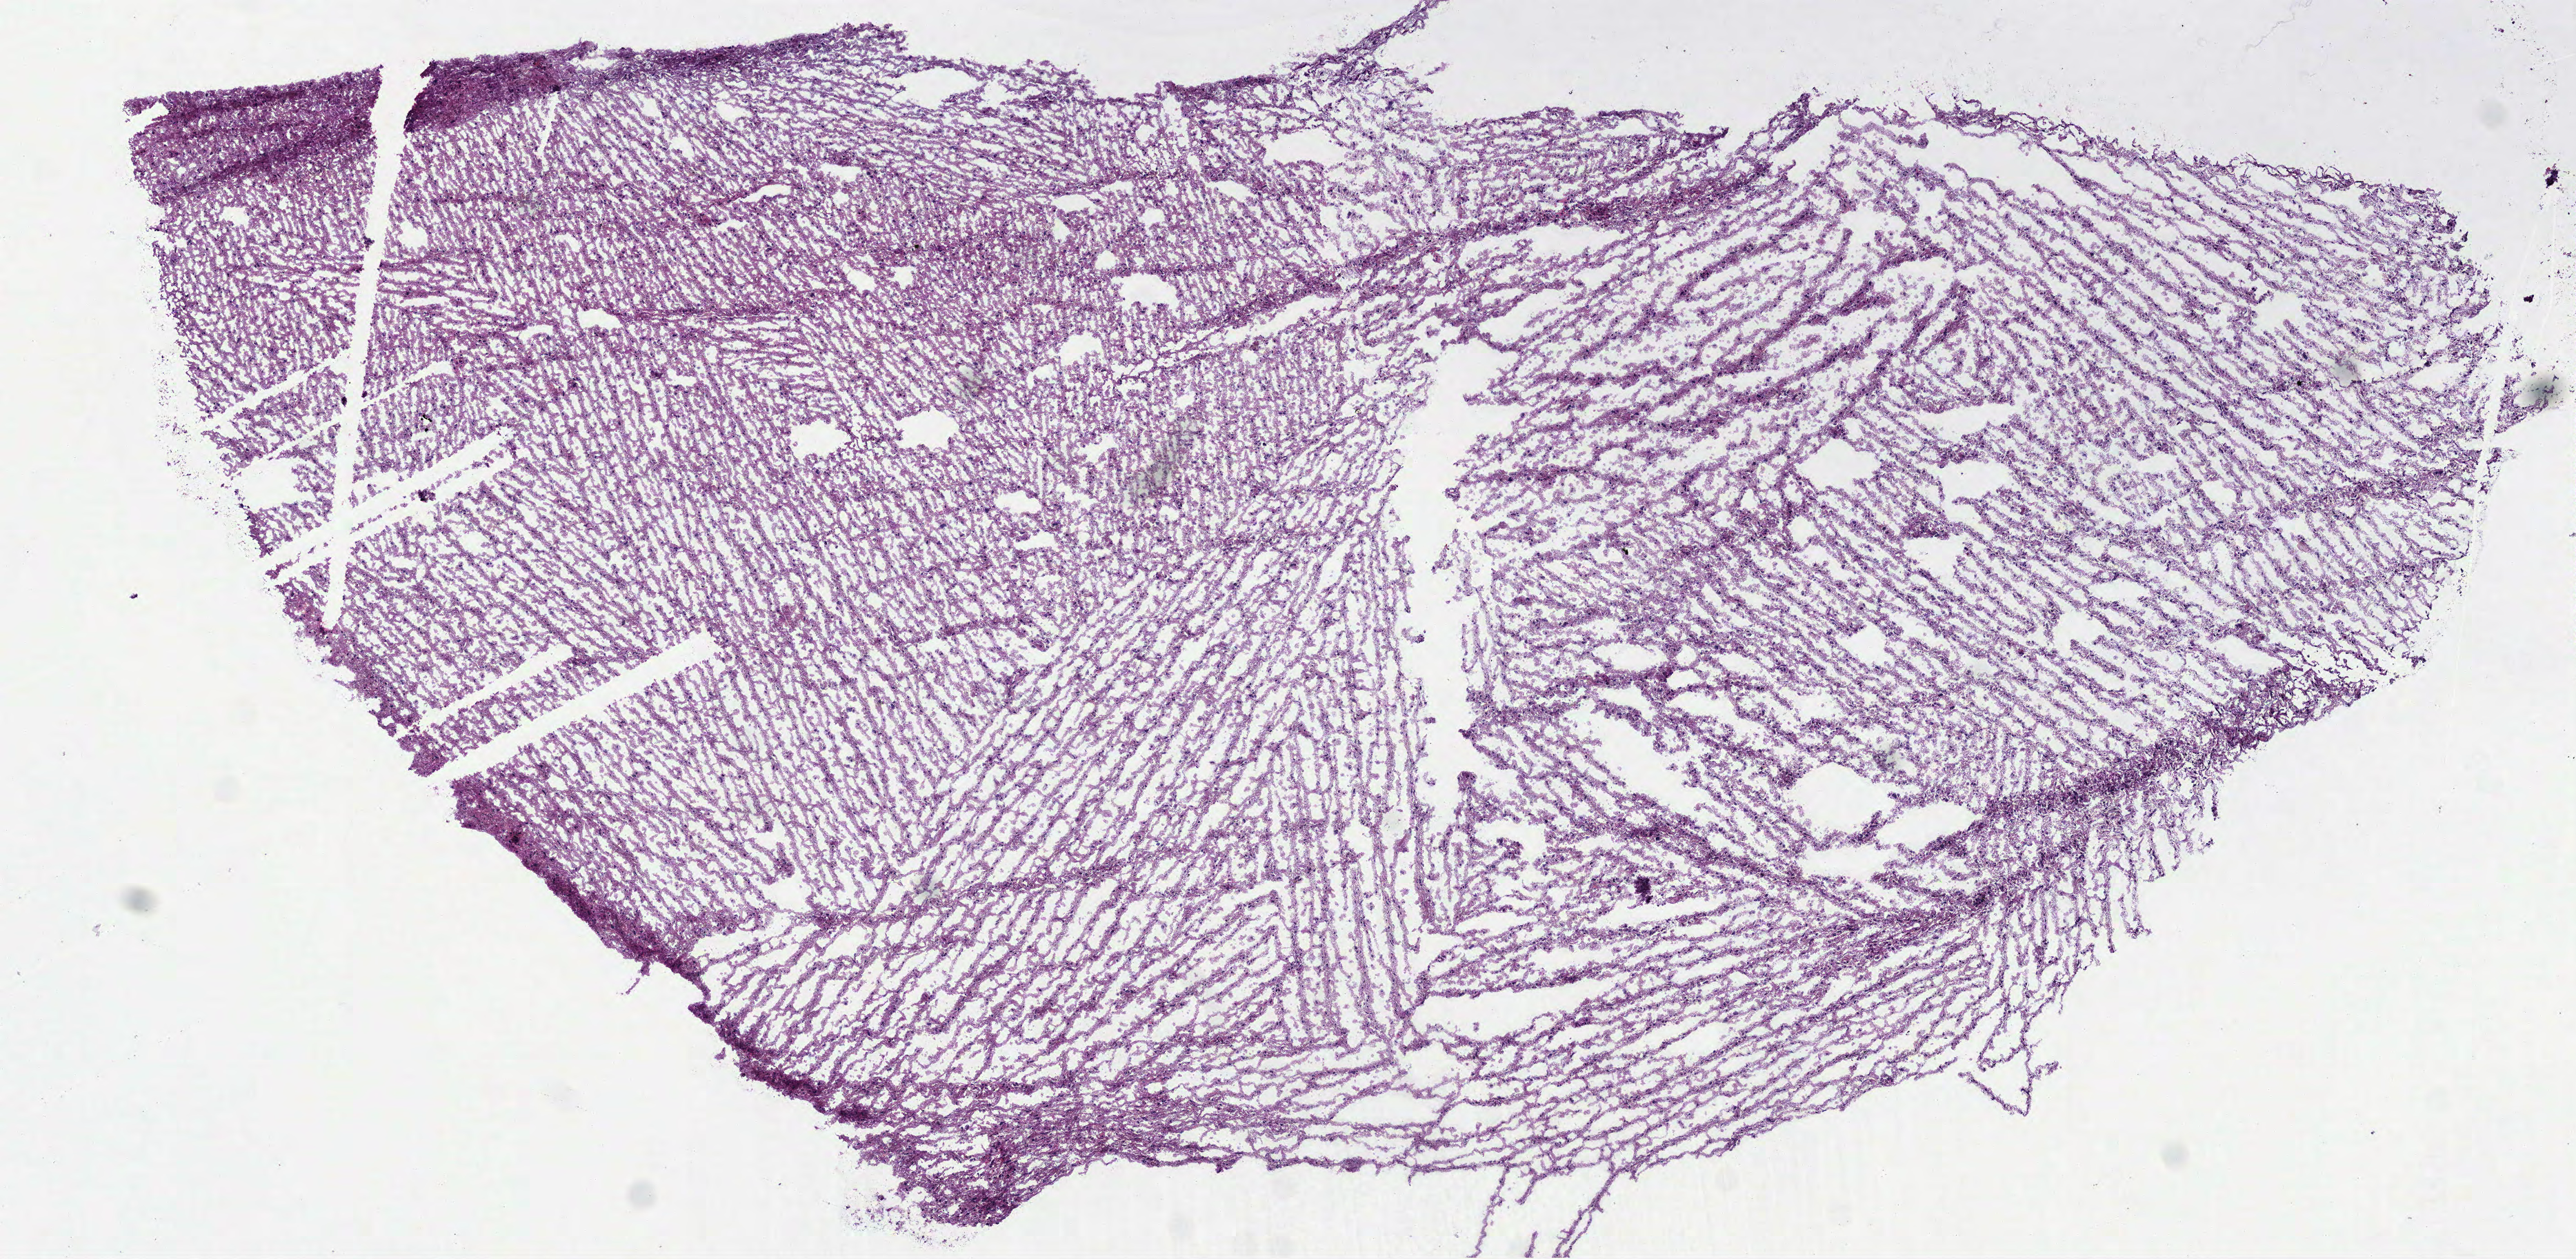
Hematoxylin and eosin (H&E) stained whole-slide image — a low-resolution overview of the entire scanned area, about 7.5 x 3.7 mm, frozen section from the bottom of the tissue portion, brain, primary tumour sample. Female patient; age at initial diagnosis 51 years. Histologic grade: G3 (poorly differentiated). Composition of this section per pathologist review: tumour cells 100%, tumour nuclei 65%, normal cells 0%, stromal cells 0%, necrosis 0%.
- laterality: right
- diagnosis: Astrocytoma, anaplastic